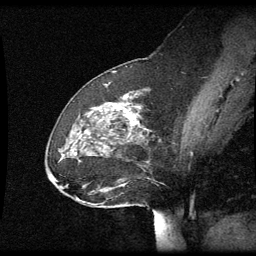
Breast MRI (dynamic contrast-enhanced), one sagittal slice; position 24 of 60 along the scan axis; dynamic contrast-enhanced series, image 2 of 3 at this slice position (ordered by acquisition); 1.5 T; TE 4.2 ms, TR 8.9 ms; 2 mm slice thickness; 256 × 256 image matrix, field of view 200 × 200 mm. Patient: female, 49 years. Case-level facts recorded for this patient, not image findings: setting: breast cancer imaged before/during neoadjuvant chemotherapy; receptor status: HR-positive, HER2-negative.
Annotated regions visible in this slice (semi-automatic segmentation, software-assisted and operator-edited):
- analysis volume of interest (the breast-tissue region the enhancement analysis was run in; not a lesion): bounding box <47,92,148,205> (left, top, right, bottom; pixels)
- tumour enhancement mask (voxels above the 70 % enhancement threshold inside the analysis volume of interest): <116,104,137,125>